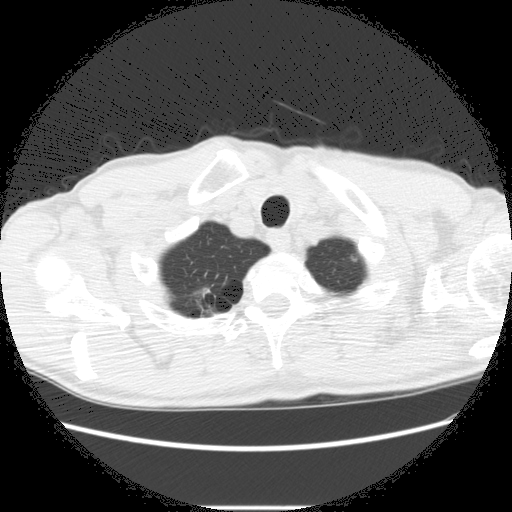
Low-dose screening chest CT, one axial slice. Slice 264 of 282 in the series (ordered by position). Reconstruction kernel STANDARD. Lung window (W 1500 / L -600 HU). 2.5 mm slice thickness. 512 × 512 image matrix.
Annotated regions visible in this slice (outlined manually by an expert reader):
- lesion 2 (nodule, upper lobe of right lung): bounding box <196,287,216,306> (left, top, right, bottom; pixels)